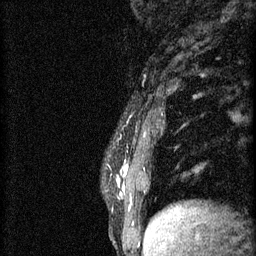
Breast MRI (dynamic contrast-enhanced), one sagittal slice. Slice 14 of 60 in the series (ordered by position). 3 images stored at this slice position (order not interpretable as contrast timing). 1.5 T. TE 4.2 ms, TR 11 ms. 2 mm slice thickness. 256 × 256 image matrix. Female patient, age 37 years.
Annotated regions visible in this slice (semi-automatic segmentation, software-assisted and operator-edited):
- analysis volume of interest (the breast-tissue region the enhancement analysis was run in; not a lesion): bounding box <117,142,171,221> (left, top, right, bottom; pixels)
- tumour enhancement mask (voxels above the 70 % enhancement threshold inside the analysis volume of interest): <117,166,128,191>